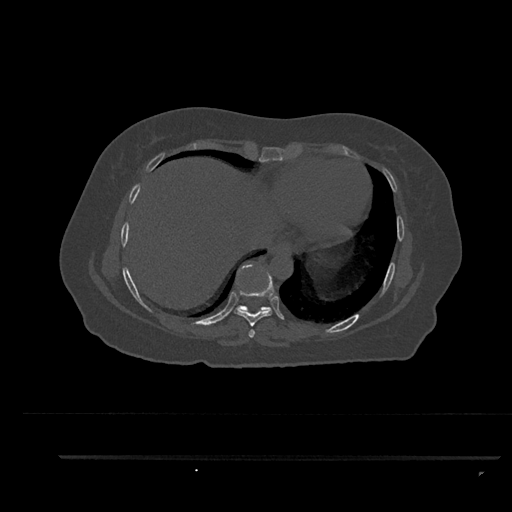
CT including the spine, one axial slice; slice 447 of 797 in the series (ordered by position); reconstruction kernel Br40s/3; bone window (W 1800 / L 400 HU); 0.5 mm slice thickness; 512 × 512 image matrix, field of view 408 × 408 mm. Female patient, age 44 years. From the clinical record (not read from this slice): primary cancer: renal; vertebrae with lytic lesions (as recorded): L1.
Outlined on this slice (semi-automatic segmentation, software-assisted and operator-edited):
- T7 vertebra: bounding box <248,329,255,338> (left, top, right, bottom; pixels)
- T8 vertebra: <234,267,274,327>
- T9 vertebra: <235,305,271,313>